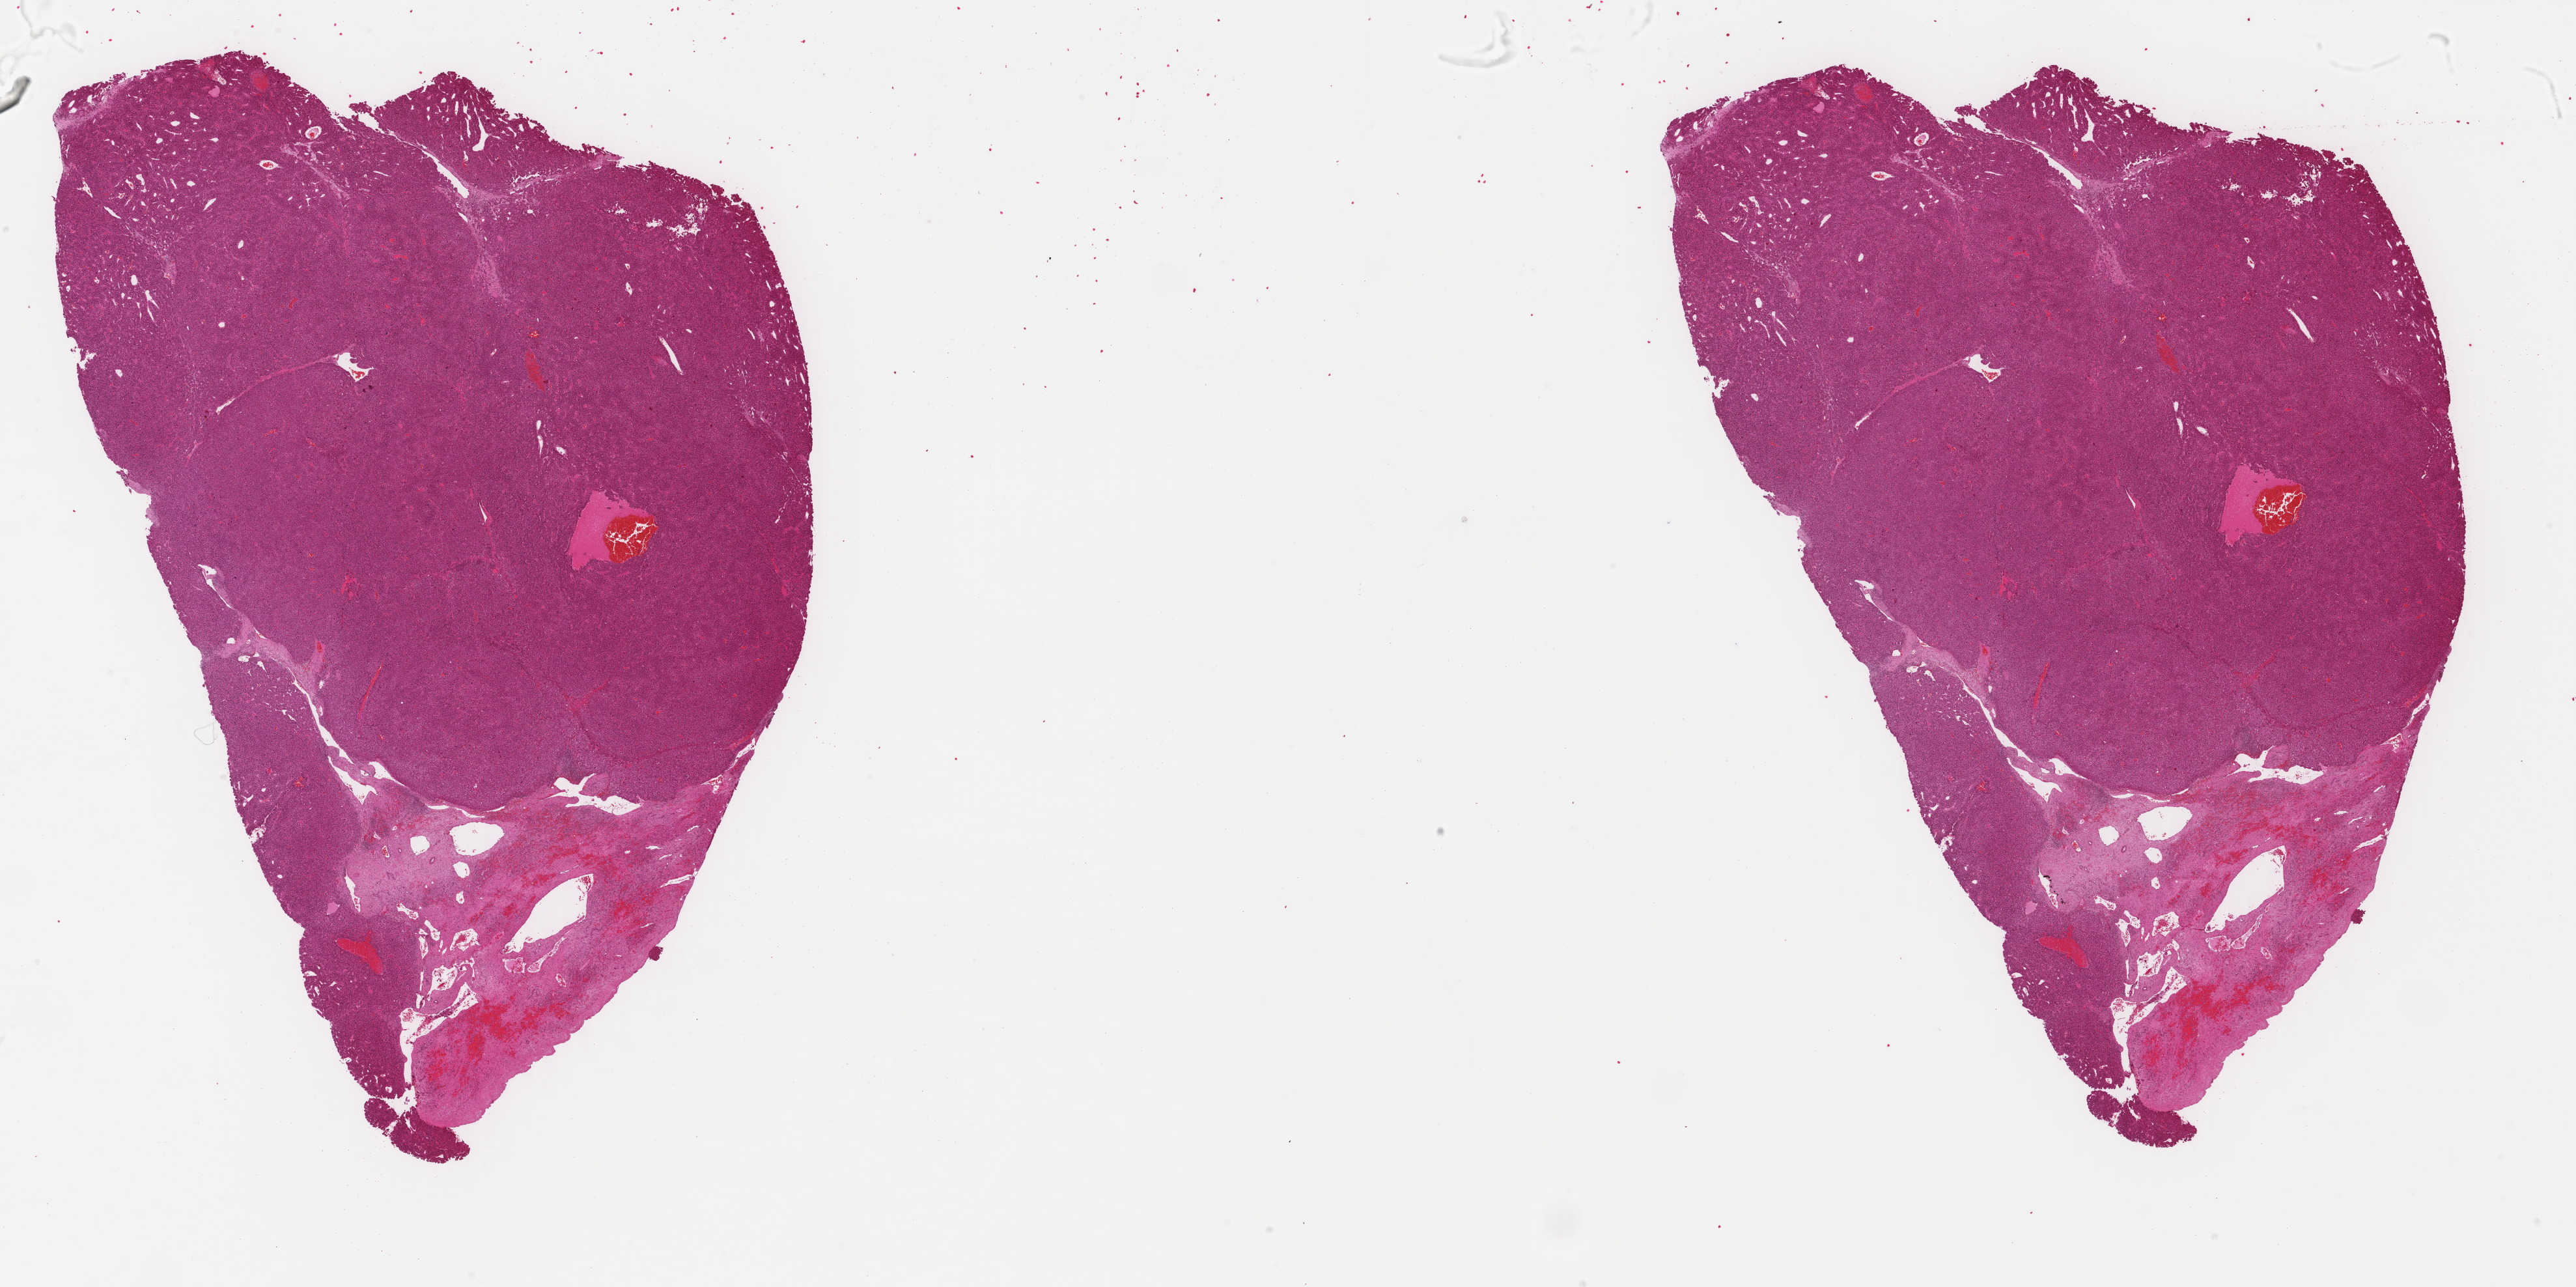
Digitized Hematoxylin and eosin (H&E) stained tissue section (whole slide), low-resolution overview of the scanned area, about 31.4 x 15.7 mm (from a 40x scan). Formalin-fixed paraffin-embedded (FFPE) diagnostic section. Sample: primary tumour, liver. Male, age 76 years at initial diagnosis.
Diagnosis: Hepatocellular carcinoma, NOS.